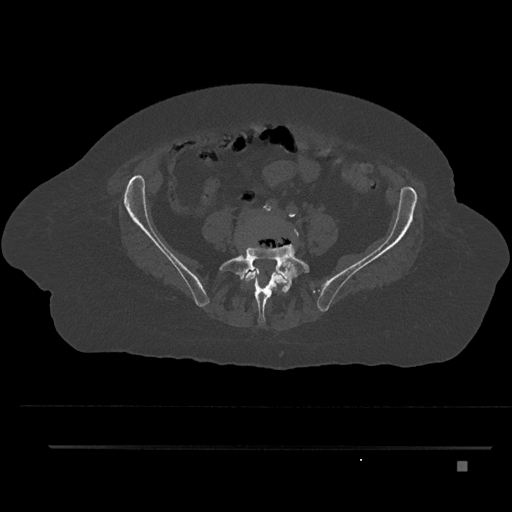
CT including the spine, one axial slice; slice 49 of 797 in the series (ordered by position); bone window (W 1800 / L 400 HU); 0.5 mm slice thickness; 512 × 512 image matrix. Patient: female, 76 years. Case-level facts recorded for this patient, not image findings: primary cancer: lung; vertebrae with lytic lesions (as recorded): T11, L3.
Outlined on this slice (semi-automatic segmentation, software-assisted and operator-edited):
- L4 vertebra: bounding box <238,221,299,307> (left, top, right, bottom; pixels)
- L5 vertebra: <219,234,310,324>